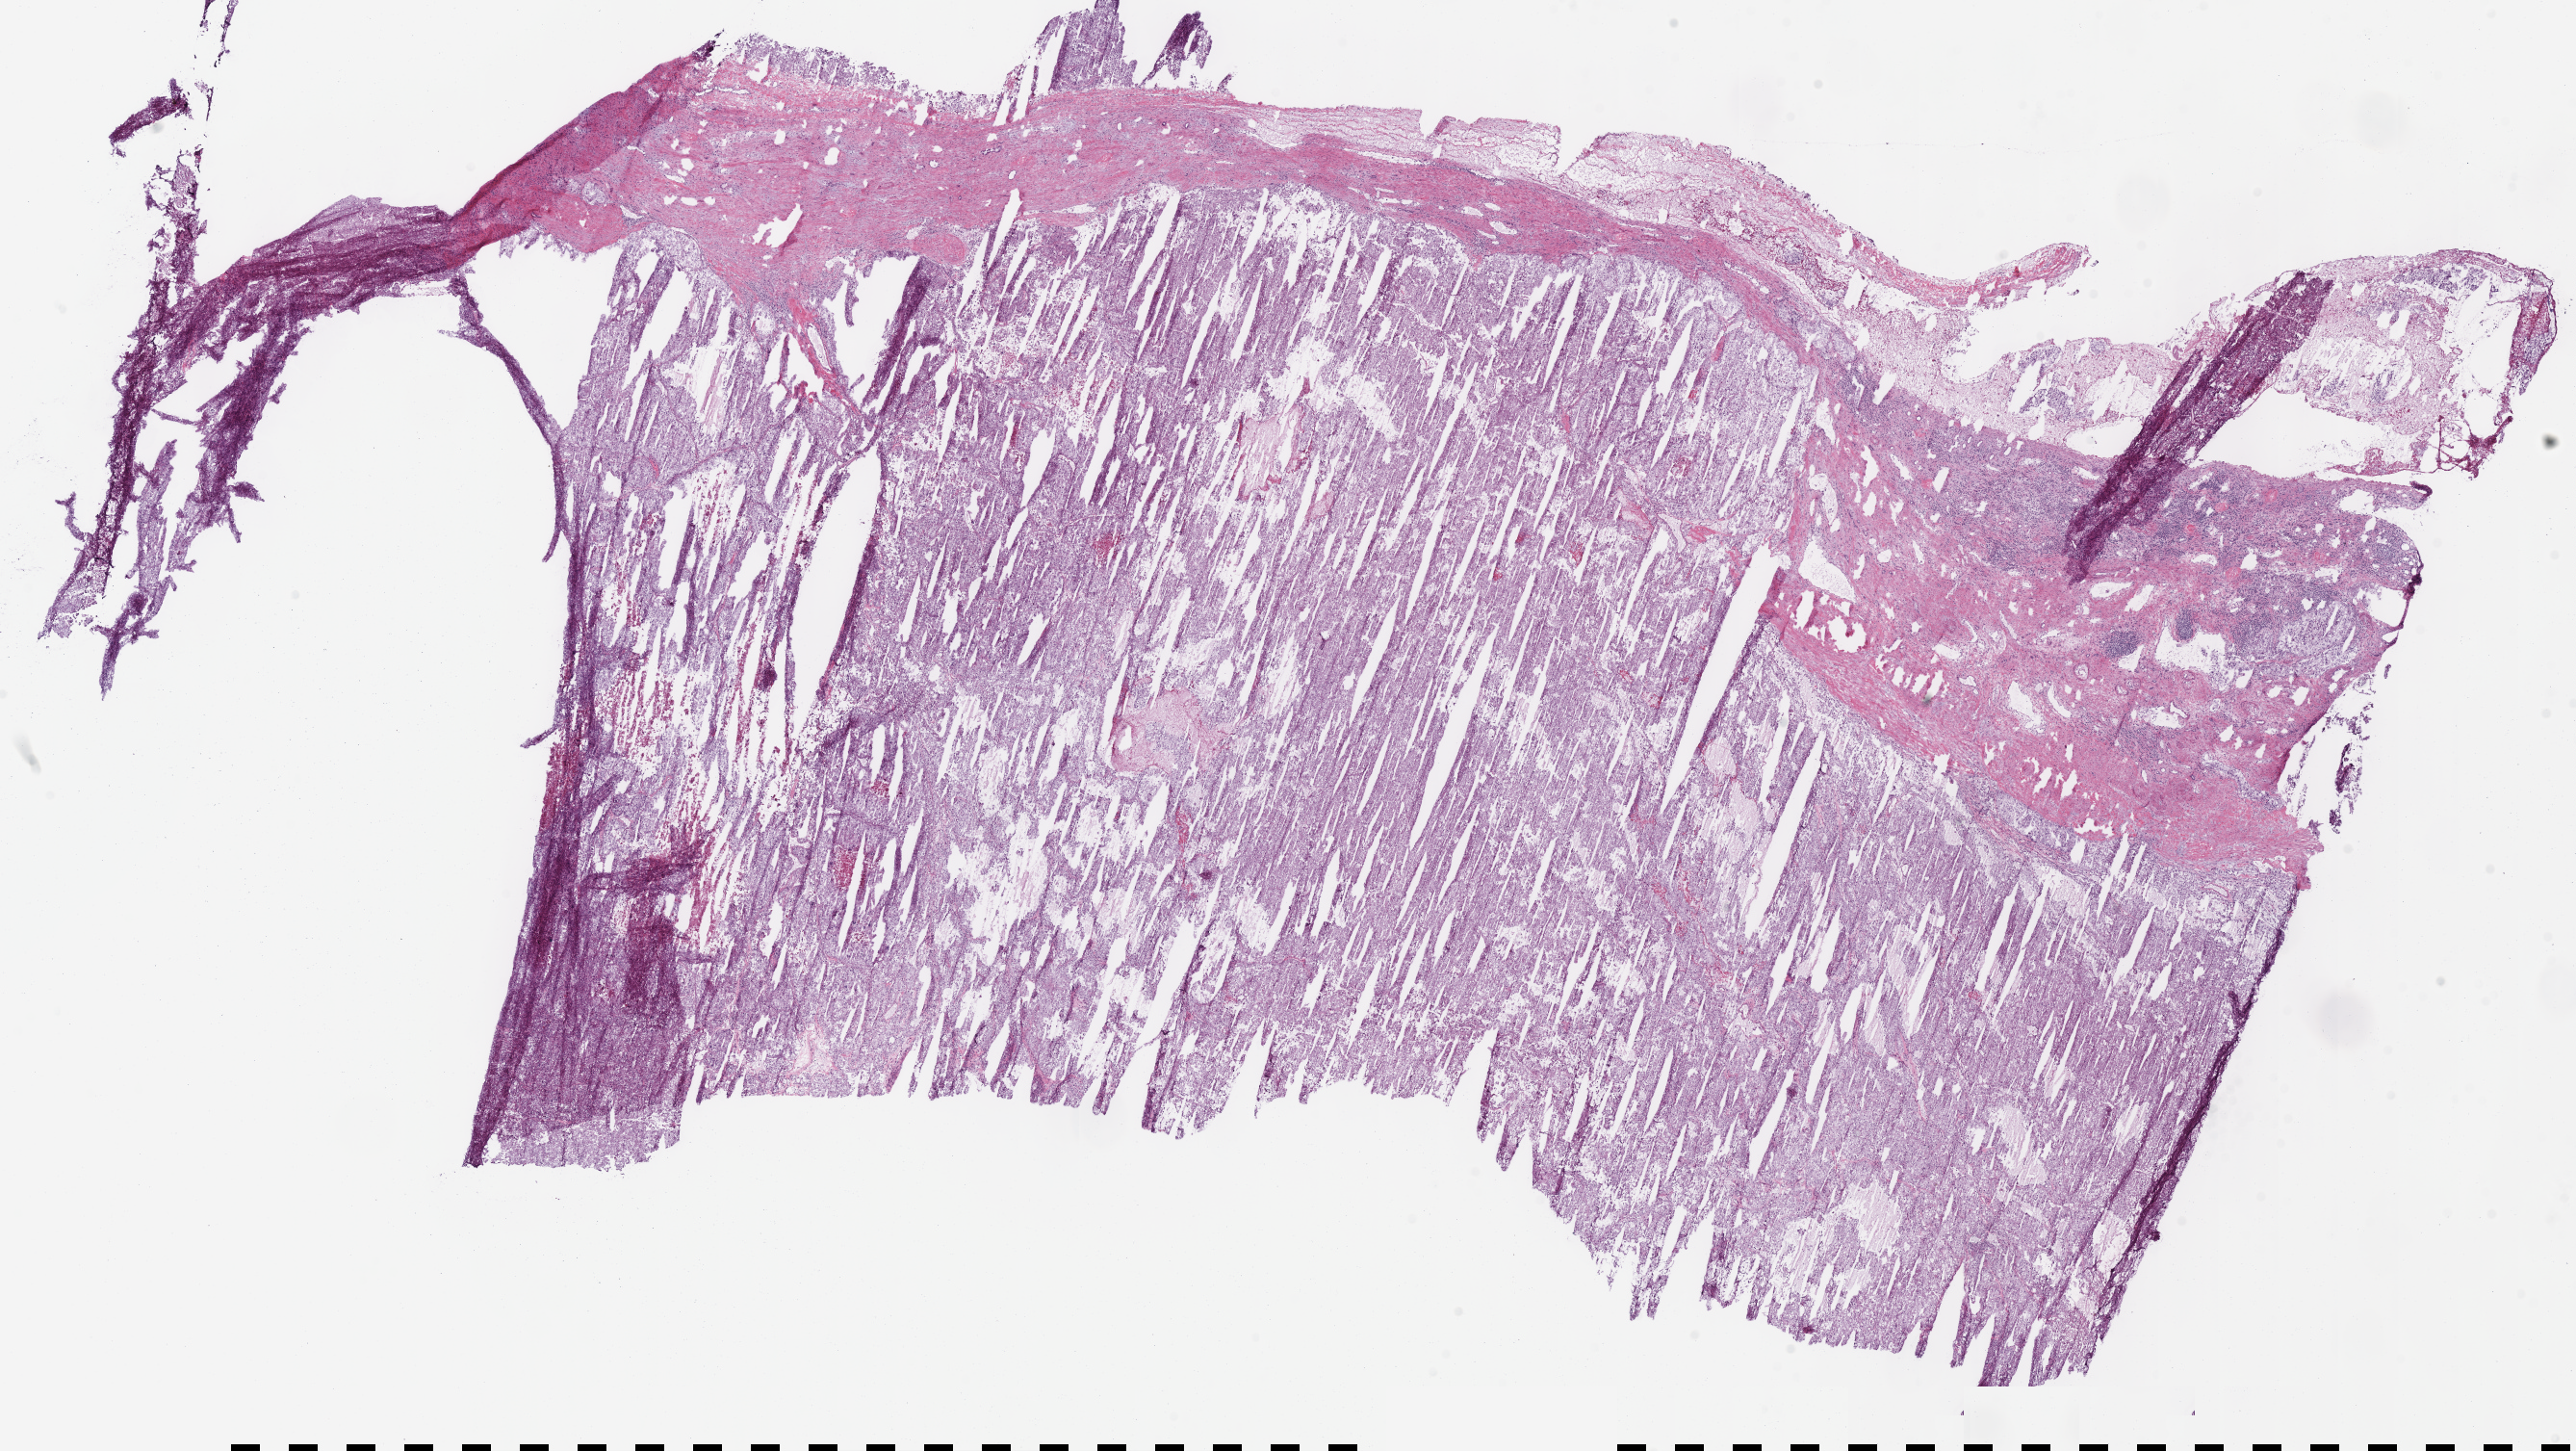
Digitized H&E-stained tissue section (whole slide), whole scanned area (about 21.0 x 11.9 mm, from a 40x scan) shown as a low-resolution overview, frozen section, sample: primary tumour, kidney. Female patient; age at initial diagnosis 51 years. Slide review estimates, as recorded: tumour cells 84%, tumour nuclei 80%, normal cells 0%, stromal cells 15%, necrosis 1%. Inflammatory infiltration, as recorded: lymphocyte infiltration 10%, monocyte infiltration 2%, neutrophil infiltration 0%.
Pathologic diagnosis: Renal cell carcinoma, chromophobe type. AJCC pathologic stage: IV (6th edition). TNM: T3b N2 M0. Laterality: right.